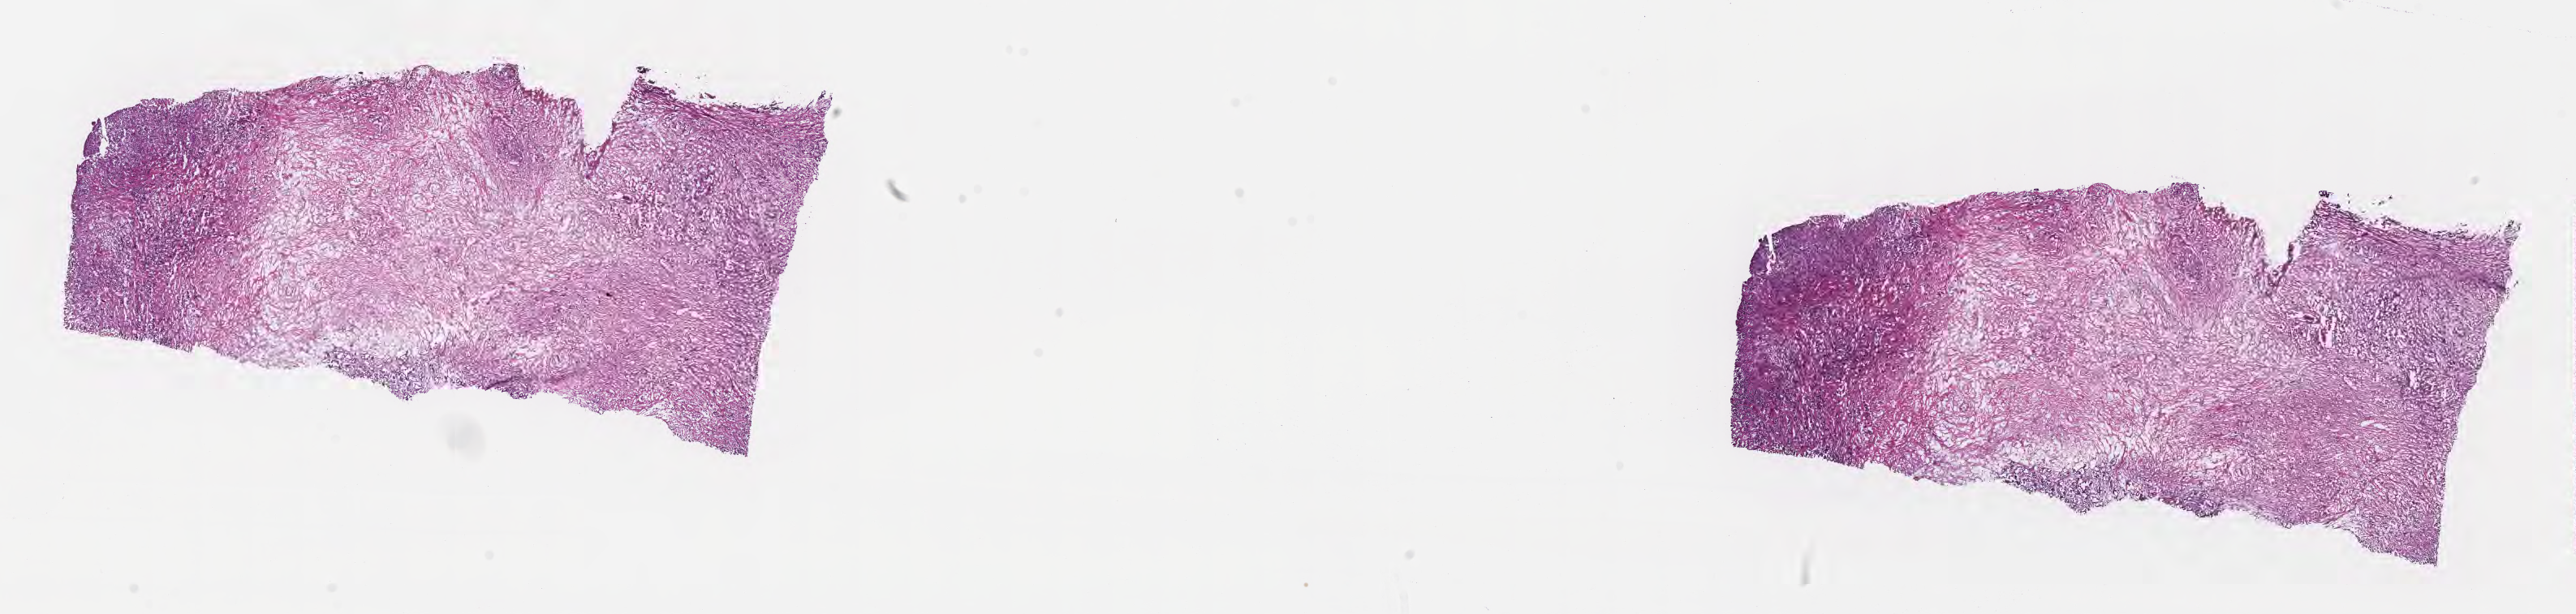
Digitized hematoxylin and eosin (H&E)-stained section, whole scanned area (about 25.7 x 6.1 mm) shown as a low-resolution overview. Cryosection. Primary tumor. Site: head of pancreas. Female, age 46 years at initial diagnosis.
Histologic diagnosis: Infiltrating duct carcinoma, NOS.